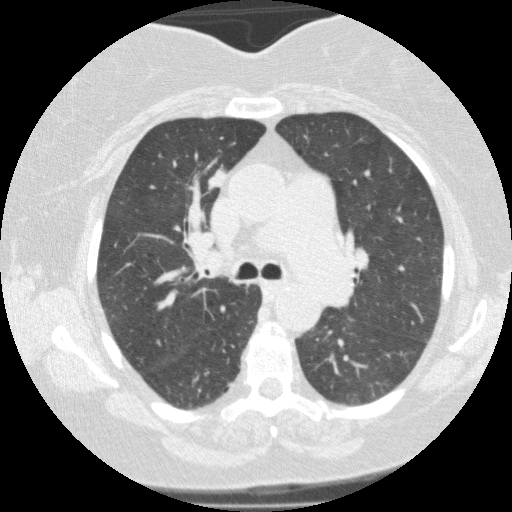
Chest CT (low-dose screening protocol), one axial image, third screening round (two years after baseline), lung window (W 1500 / L -600 HU), 2 mm slice thickness, standard (soft-tissue) reconstruction kernel (FC01), 120 kVp, slice 54 of 146 in the series, 512 × 512 image matrix. Female, age 62 years at enrolment. Current smoker at enrolment.
Expert-annotated lung lesion, bounding box <189,158,235,200> (left, top, right, bottom; pixels). The screening reader recorded 5 non-calcified nodules or masses ≥4 mm on this exam; which of them this box marks is not recorded. Lung cancer was diagnosed 76 days after this screen: adenocarcinoma, NOS, right upper lobe, poorly differentiated (G3), stage IB (AJCC 6th edition), 12 mm at pathology.